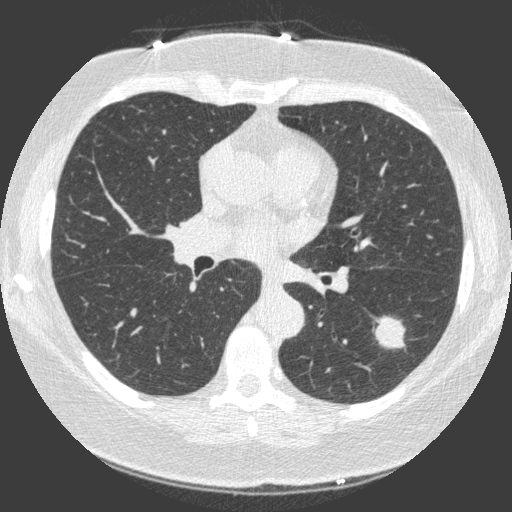
Axial slice from a low-dose chest CT screening exam; third screening round (two years after baseline); lung window (W 1500 / L -600 HU); 120 kVp; slice 63 of 149 in the series; 512 × 512 image matrix, field of view 330 × 330 mm. Female participant, aged 66 years at enrolment. Current smoker at enrolment.
Expert-annotated lung lesion, bounding box <364,302,420,353> (left, top, right, bottom; pixels). The exam's reader record, not a measurement of the box and not confirmed to be the same lesion: non-calcified nodule or mass ≥4 mm, left lower lobe, 23 × 17 mm, spiculated (stellate) margins, soft tissue attenuation, pre-existing on the prior screen: yes; interval growth: yes.